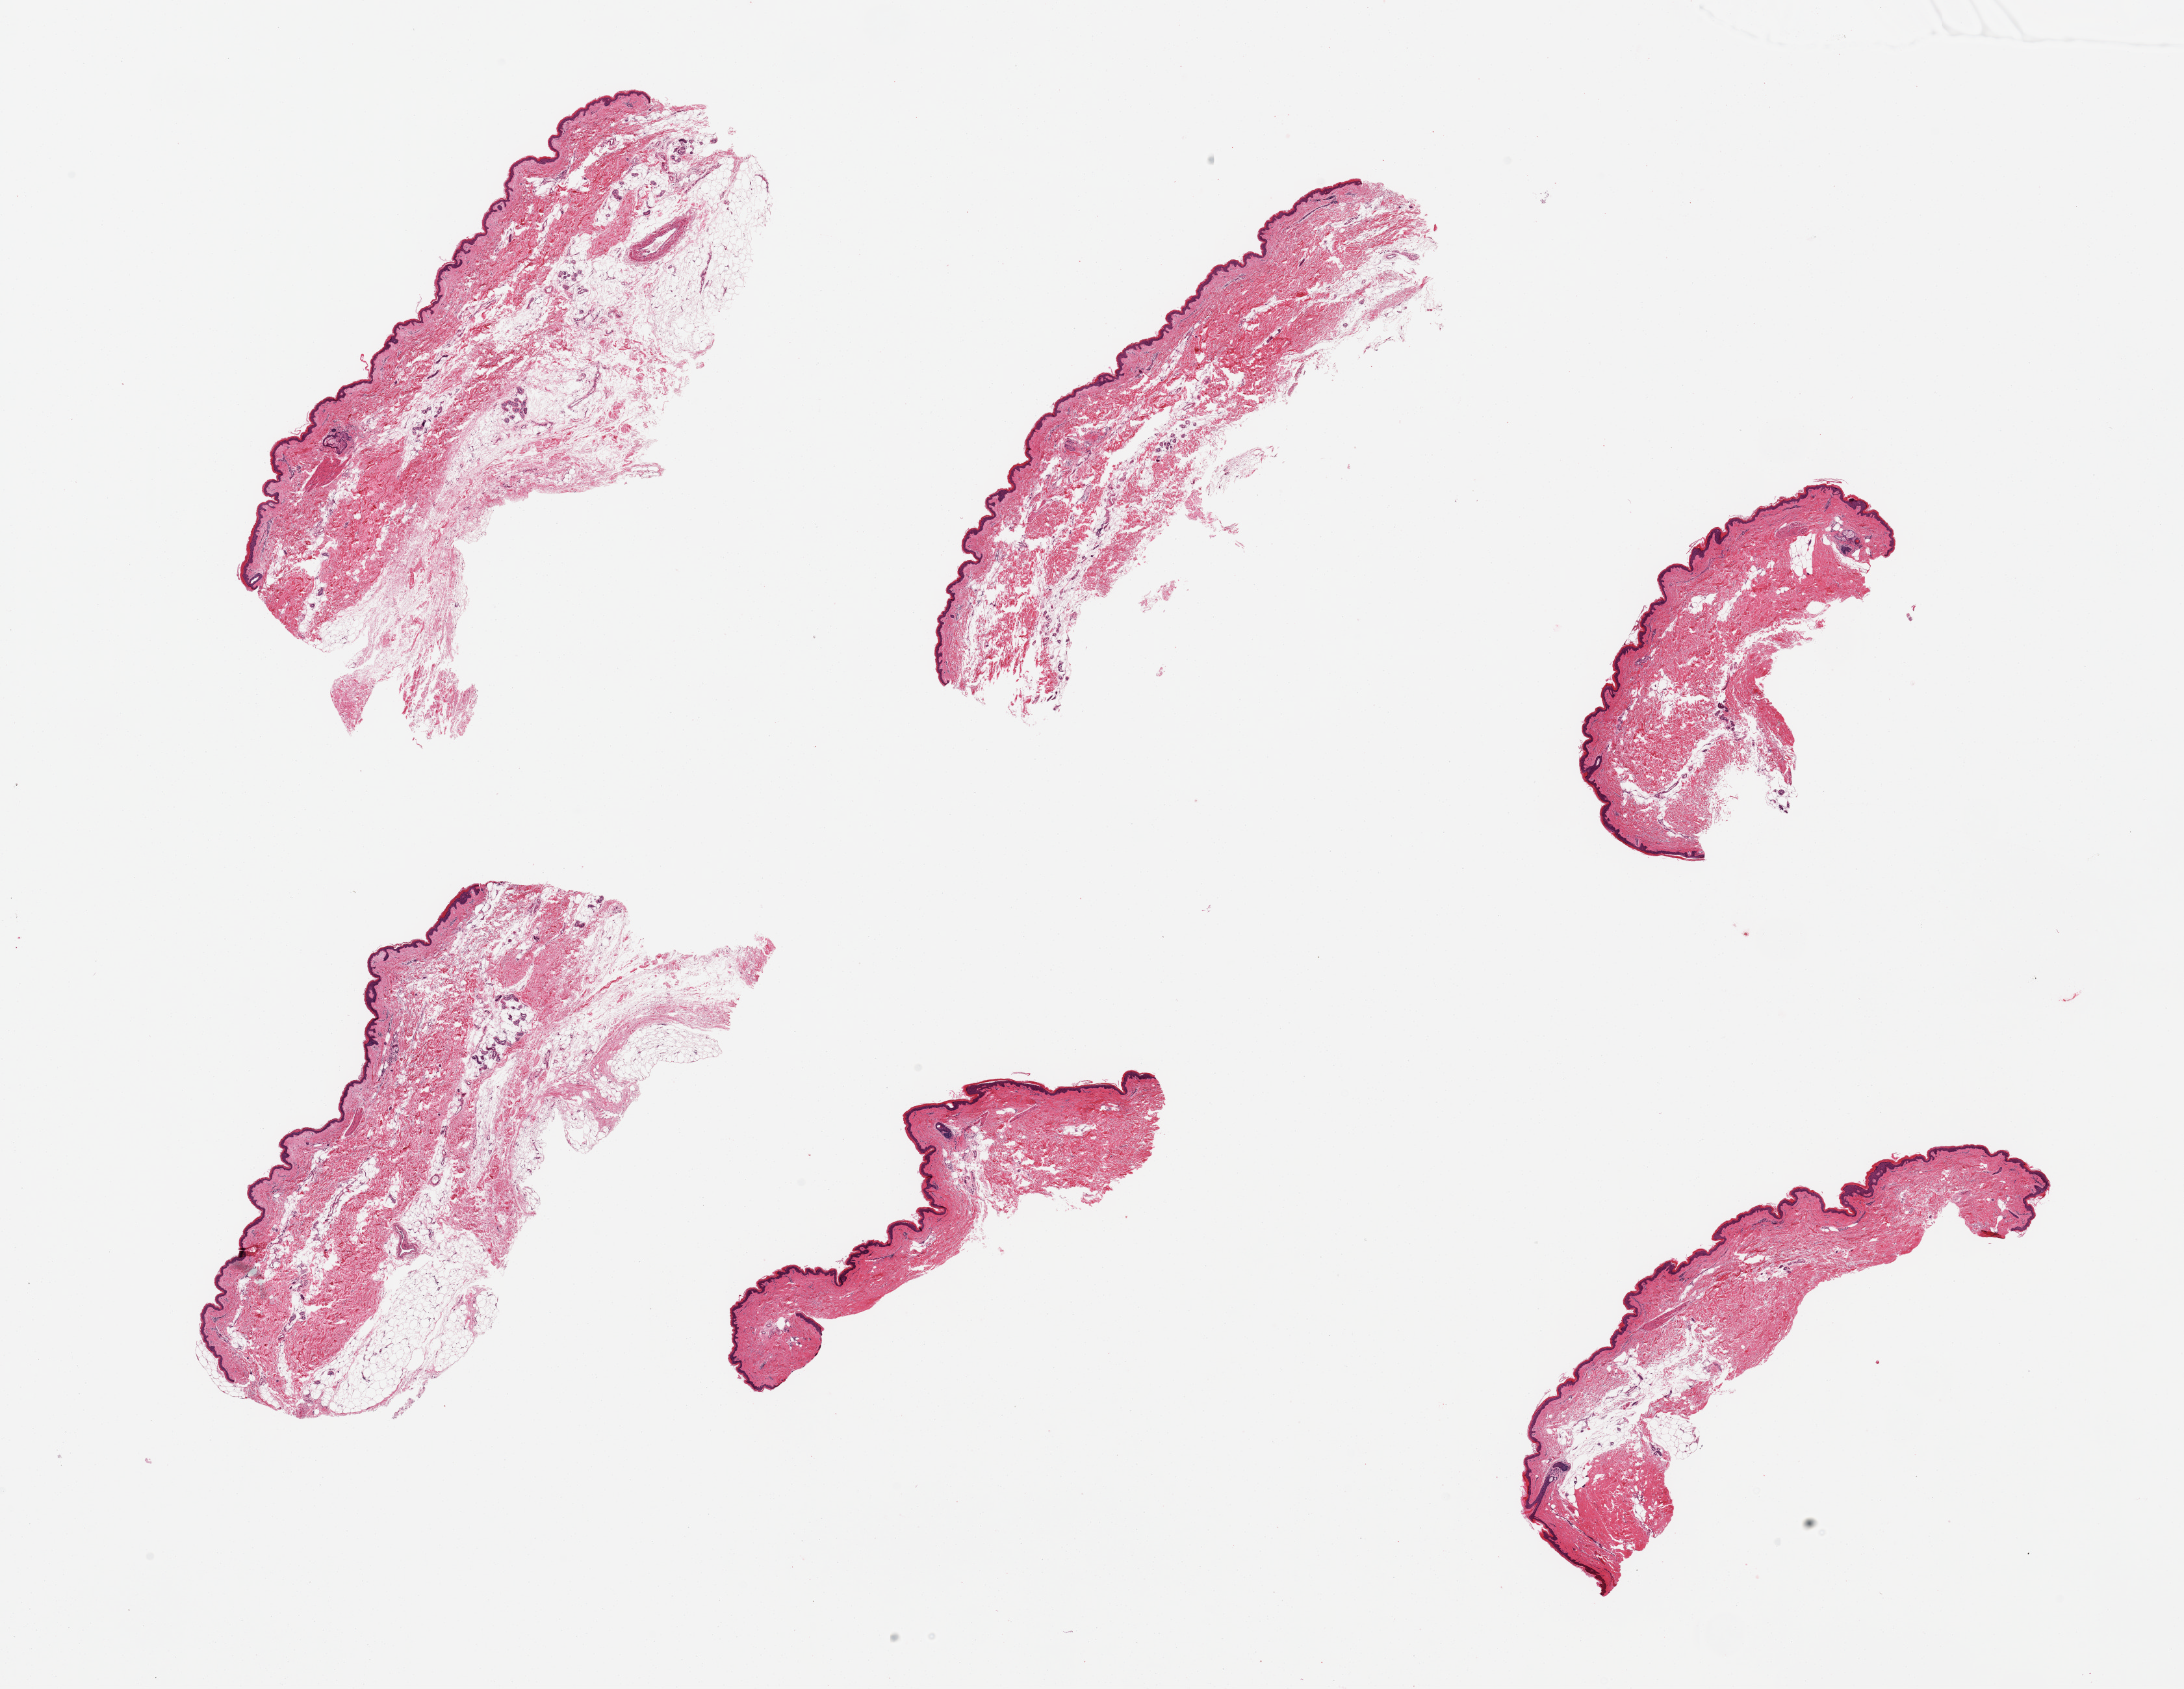
Digitized H&E-stained section, brightfield — low-resolution overview of the scanned area, about 26.6 x 20.6 mm. PAXgene-fixed paraffin-embedded (PFPE) section. Sampled site (target tissue): skin of lower leg. Tissue donor sample. Donor sex: female.
• reviewer comment on this tissue sample: 6 pieces, squamous epithelium is ~30 microns; adherent dermal fat focallky present up to ~1.5mm